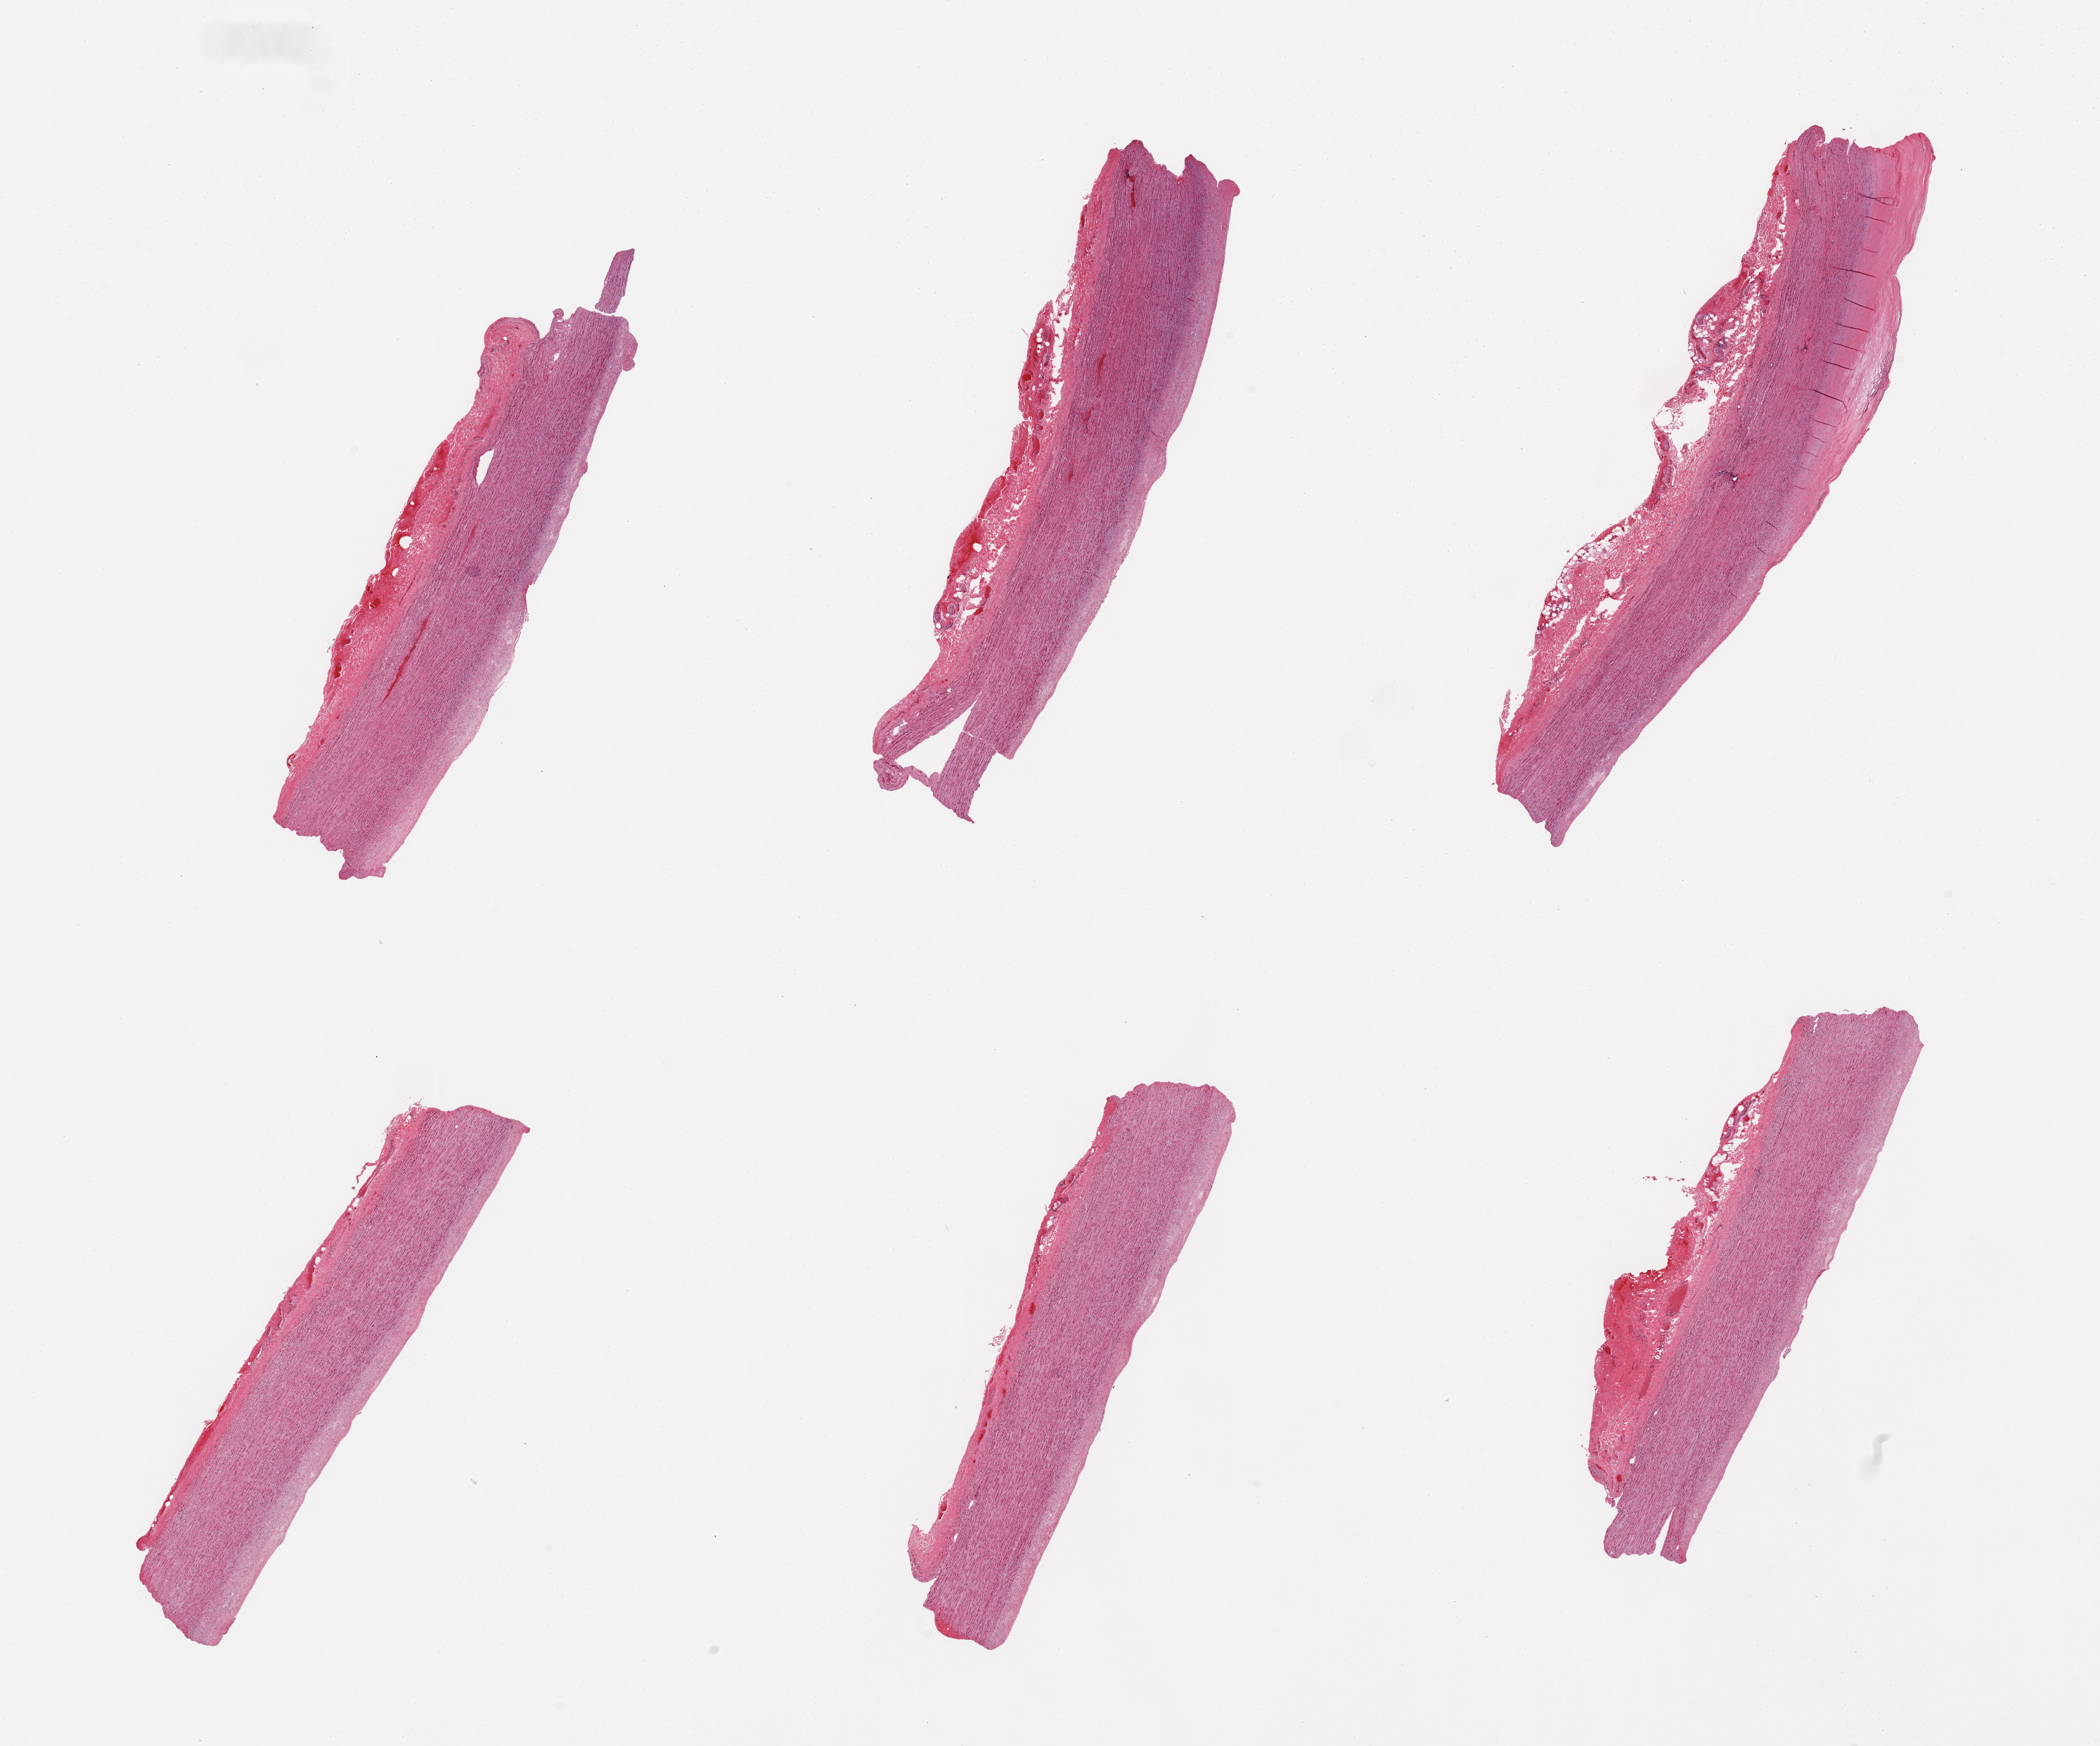
Digitized H&E-stained section, whole scanned area (about 23.6 x 19.6 mm) shown as a low-resolution overview. PAXgene-fixed, paraffin-embedded tissue. Target tissue: aorta. Donor tissue sample.
• review note (as recorded): 2 pieces, atherosis up to ~0.7mm